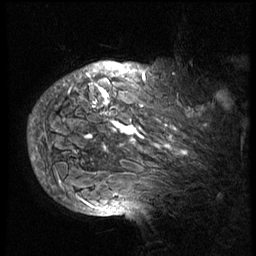
Breast MRI (dynamic contrast-enhanced), one sagittal slice. Slice 59 of 74 in the series (ordered by position). 3 images stored at this slice position (order not interpretable as contrast timing). 1.5 T. TE 4.2 ms, TR 8.9 ms. 256 × 256 image matrix, field of view 200 × 200 mm. Patient: female, 57 years. From the clinical record (not read from this slice): setting: breast cancer imaged before/during neoadjuvant chemotherapy; receptor status: HER2-positive.
Outlined on this slice (semi-automatically segmented with operator editing):
- analysis volume of interest (the breast-tissue region the enhancement analysis was run in; not a lesion): box from (x=40, y=62) to (x=238, y=175) px
- tumour enhancement mask (voxels above the 140 % enhancement threshold inside the analysis volume of interest): (x=40, y=68)–(x=189, y=175)